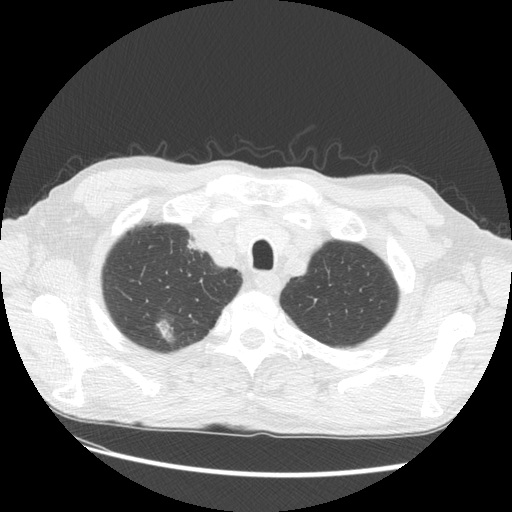
Low-dose screening chest CT, one axial slice; position 119 of 133 along the scan axis; lung window (W 1500 / L -600 HU); 2.5 mm slice thickness; 512 × 512 image matrix.
Annotated regions visible in this slice (expert manual segmentation):
- lesion 2 (tumor, upper lobe of right lung): bounding box <156,319,175,342> (left, top, right, bottom; pixels)